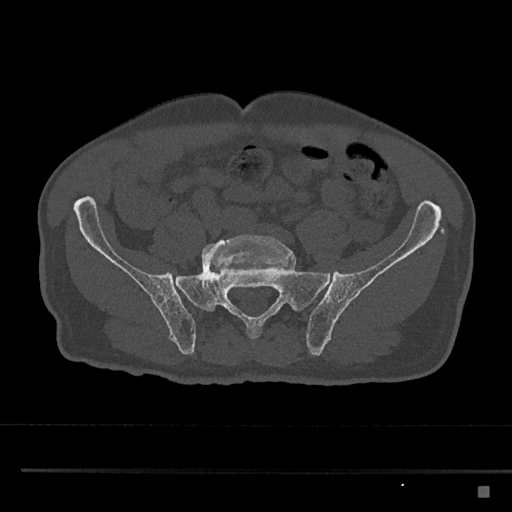
CT including the spine, one axial slice; position 546 of 797 along the scan axis; reconstruction kernel Br40s/3; bone window (W 1800 / L 400 HU); 0.5 mm slice thickness; 512 × 512 image matrix, field of view 391 × 391 mm. Male patient, age 59 years. From the clinical record (not read from this slice): primary cancer: prostate.
Structures marked on this image (semi-automatic segmentation, software-assisted and operator-edited):
- L5 vertebra: bounding box [x1, y1, x2, y2] px = [201, 235, 292, 273]